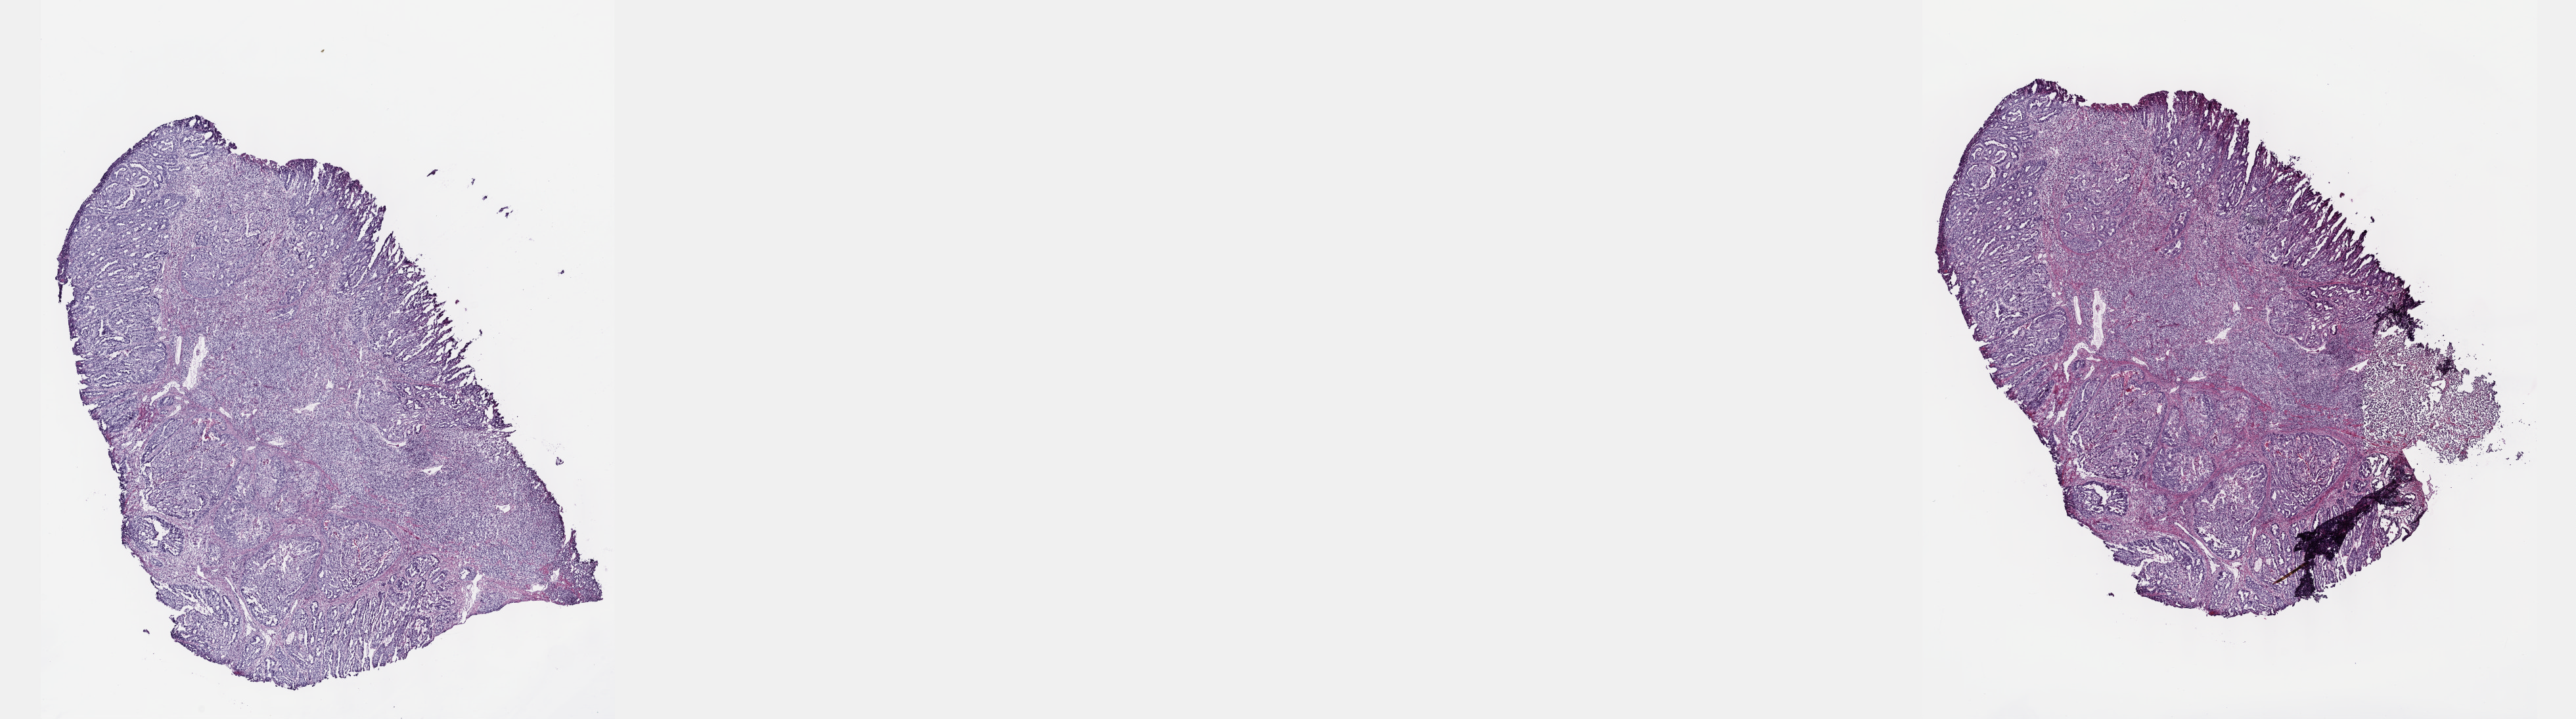
H&E whole-slide image — low-resolution overview of the scanned area, about 31.7 x 8.8 mm; frozen section from the top of the tissue portion; sample: primary tumour, stomach. Male patient; age at initial diagnosis 70 years. Histologic grade: G3 (poorly differentiated). Slide review estimates, as recorded: tumour cells 80%, tumour nuclei 80%, normal cells 0%, stromal cells 20%, necrosis 0%. Inflammatory infiltration, as recorded: lymphocyte infiltration 40%, monocyte infiltration 20%, neutrophil infiltration 20%.
Pathologic diagnosis: Signet ring cell carcinoma. AJCC pathologic stage: IV (7th edition).